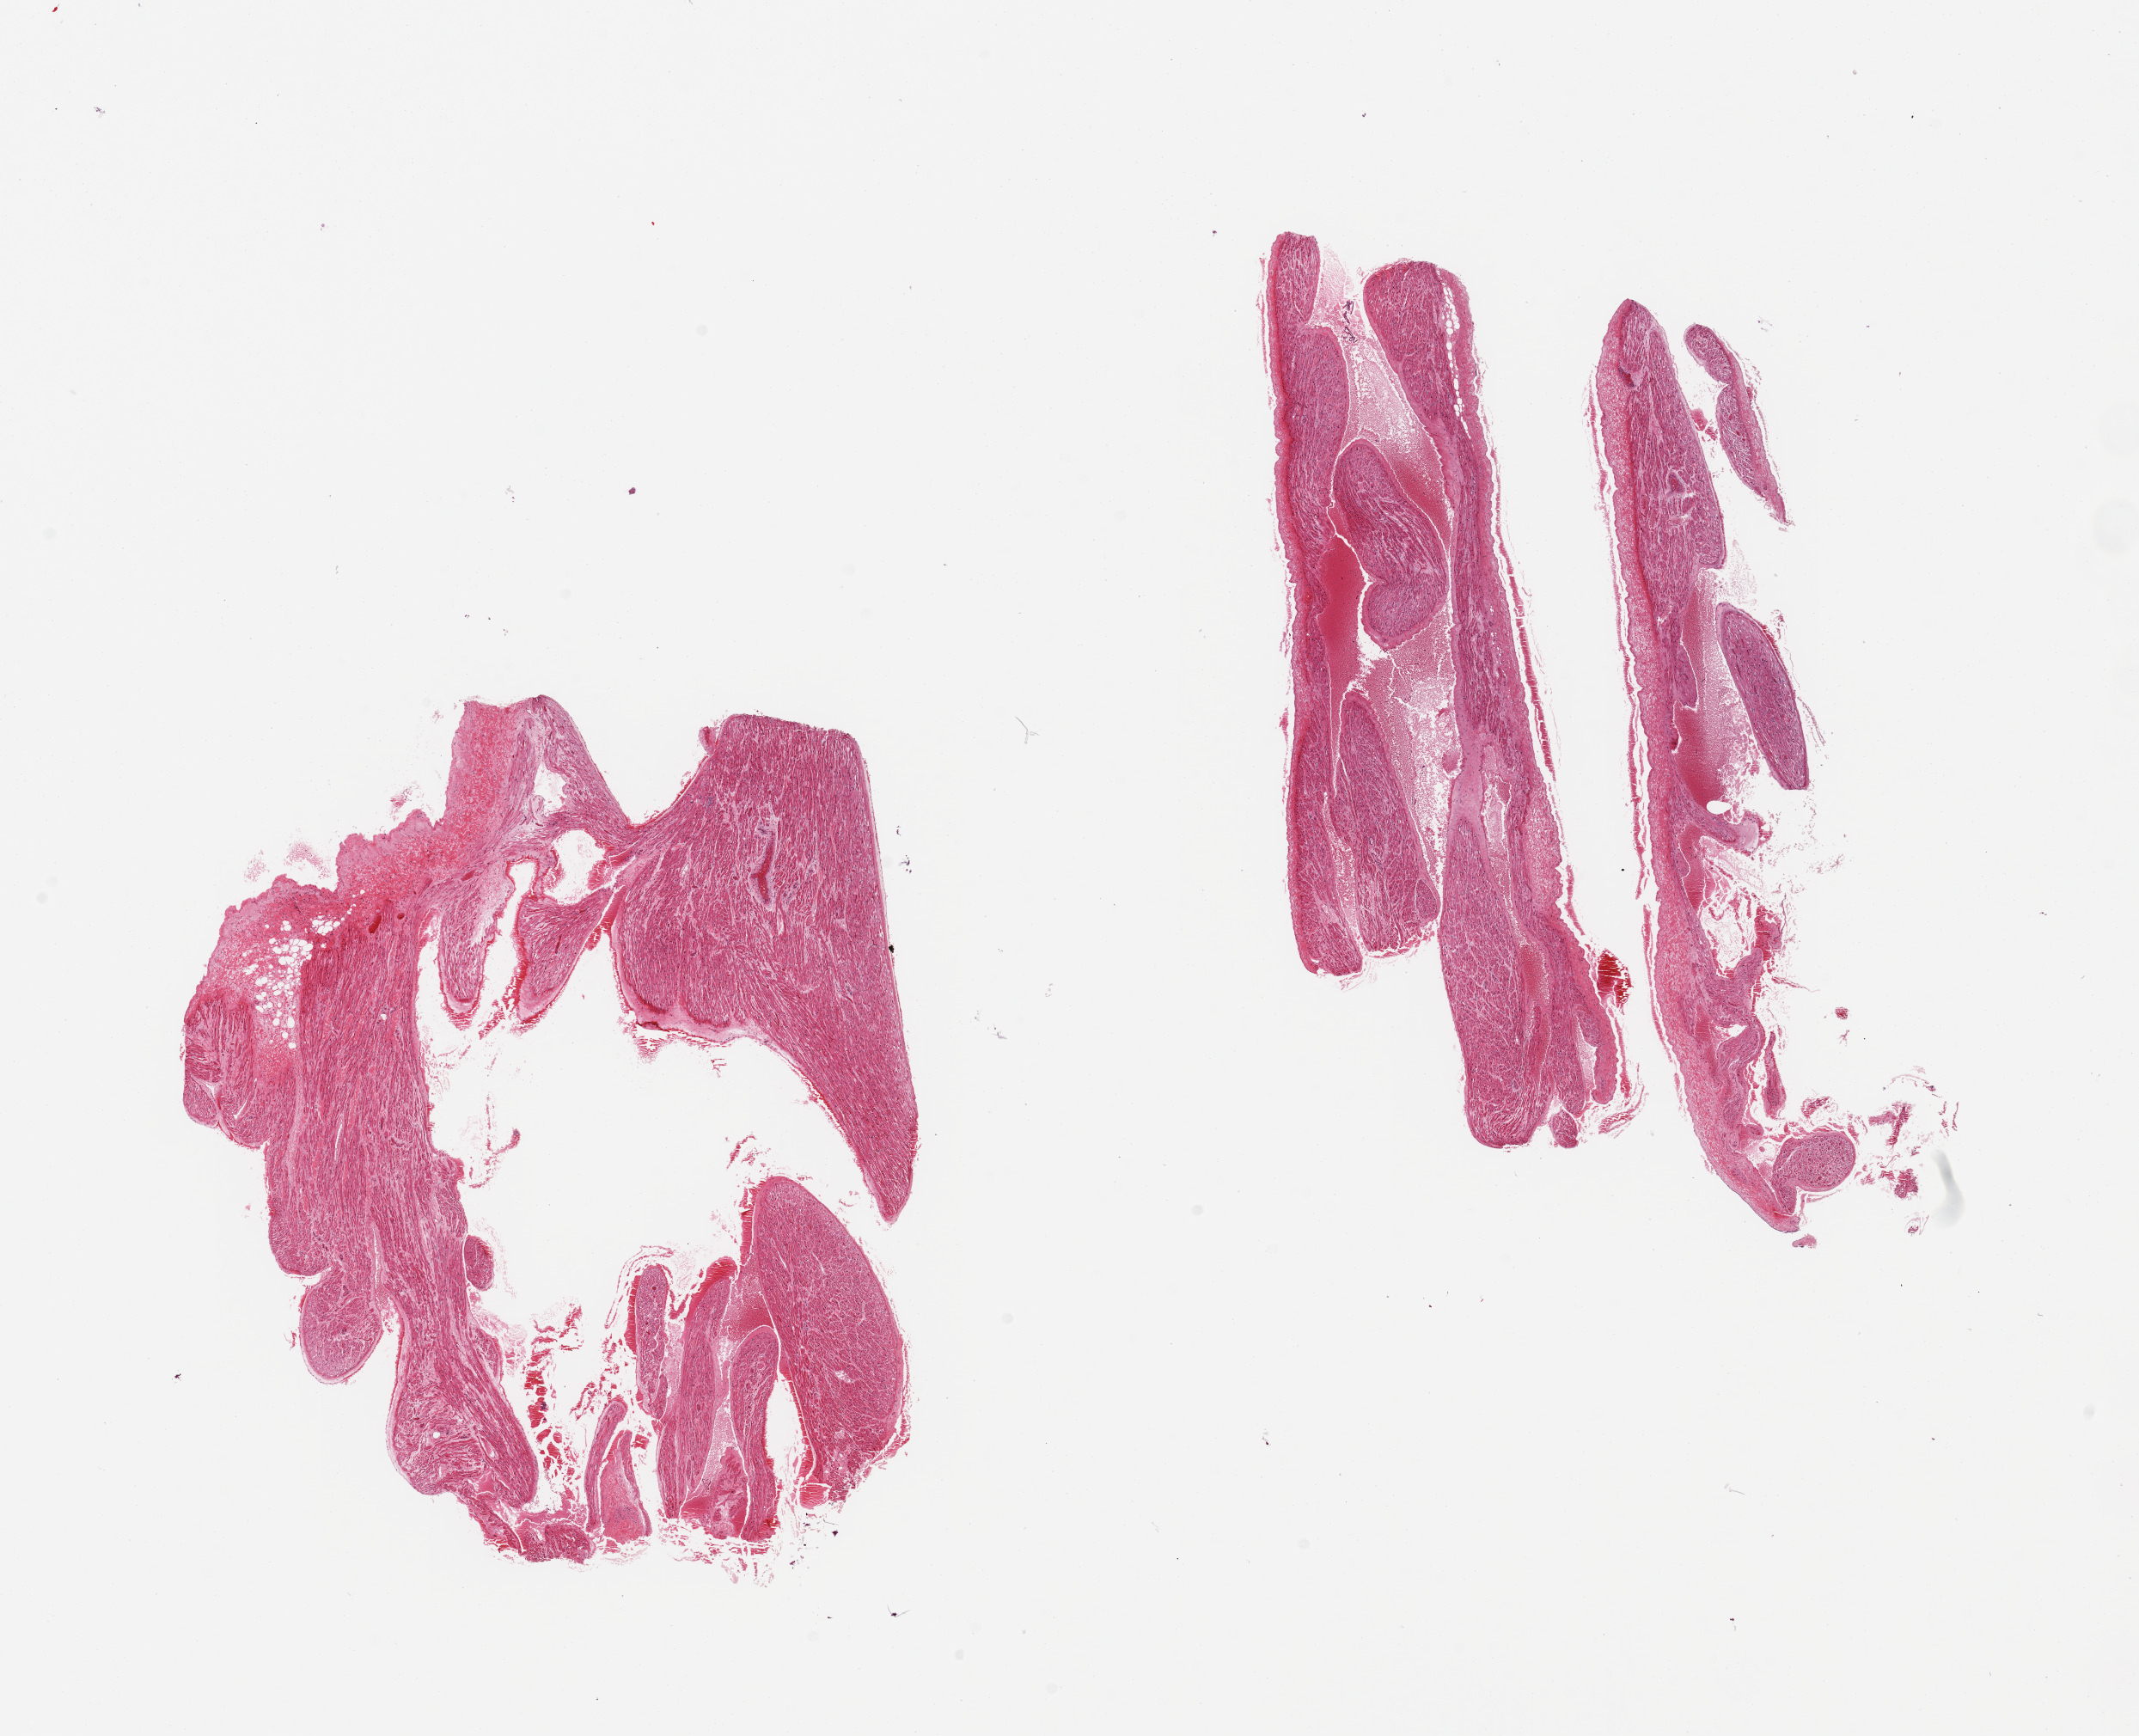
Digitized haematoxylin and eosin-stained section — whole scanned area (about 19.7 x 16.0 mm, acquisition: 20x scan) shown as a low-resolution overview; PAXgene-fixed paraffin-embedded (PFPE) section; section of auricular appendage (target tissue); donor tissue sample. Male donor.
• pathologist's review note for this sample: 2 pieces, large central defects in both pieces